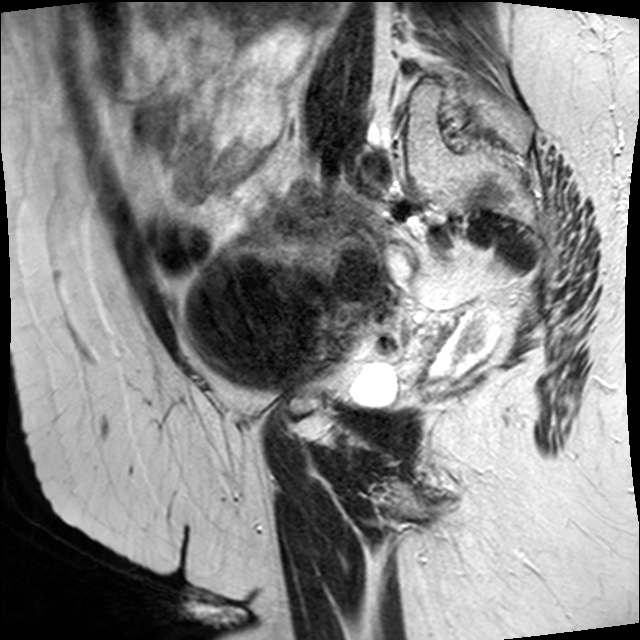
Pelvic MRI for cervical cancer, one sagittal slice. Slice 15 of 45 in the series (ordered by position). T2-weighted. 1.5 T. TE 89 ms, TR 4610 ms. 4 mm slice thickness. 640 × 640 image matrix. Female patient, age 50 years.
Outlined on this slice (manually delineated by an expert):
- uterus and cervix: bounding box <181,242,475,383> (left, top, right, bottom; pixels)